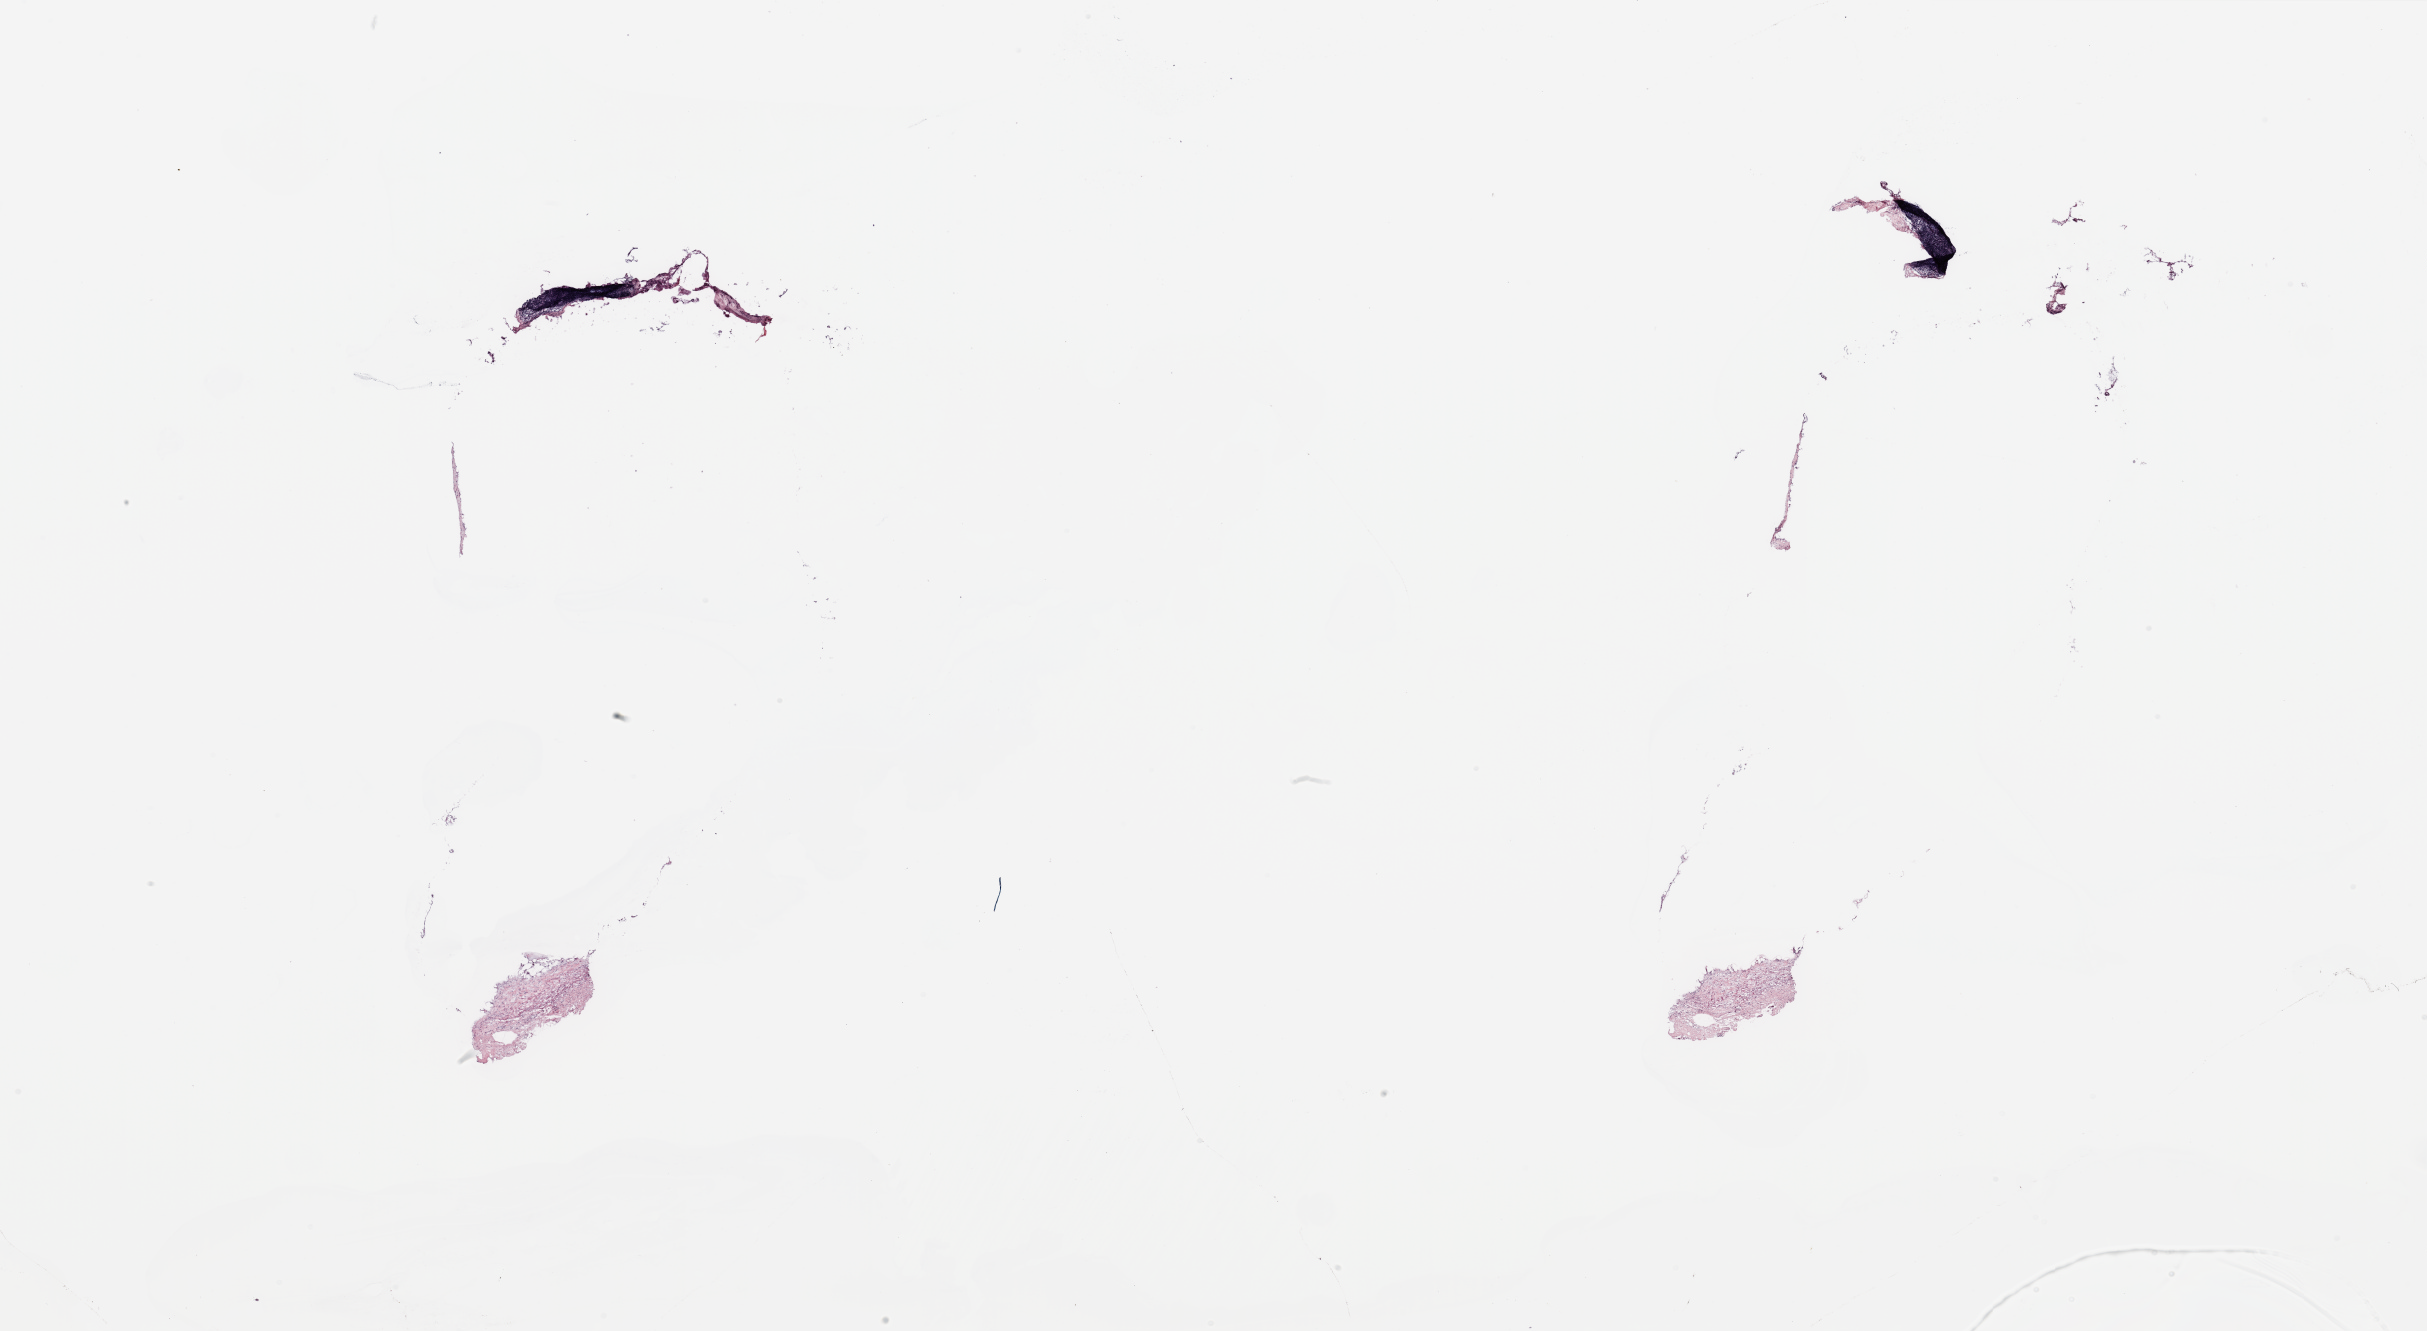
Digitized H&E tissue section (whole slide) — a low-resolution overview of the entire scanned area, about 38.4 x 21.1 mm (slide scanned at 20x). Breast, tissue type not recorded.
Patient diagnosis (cohort enrolment): breast cancer (breast).